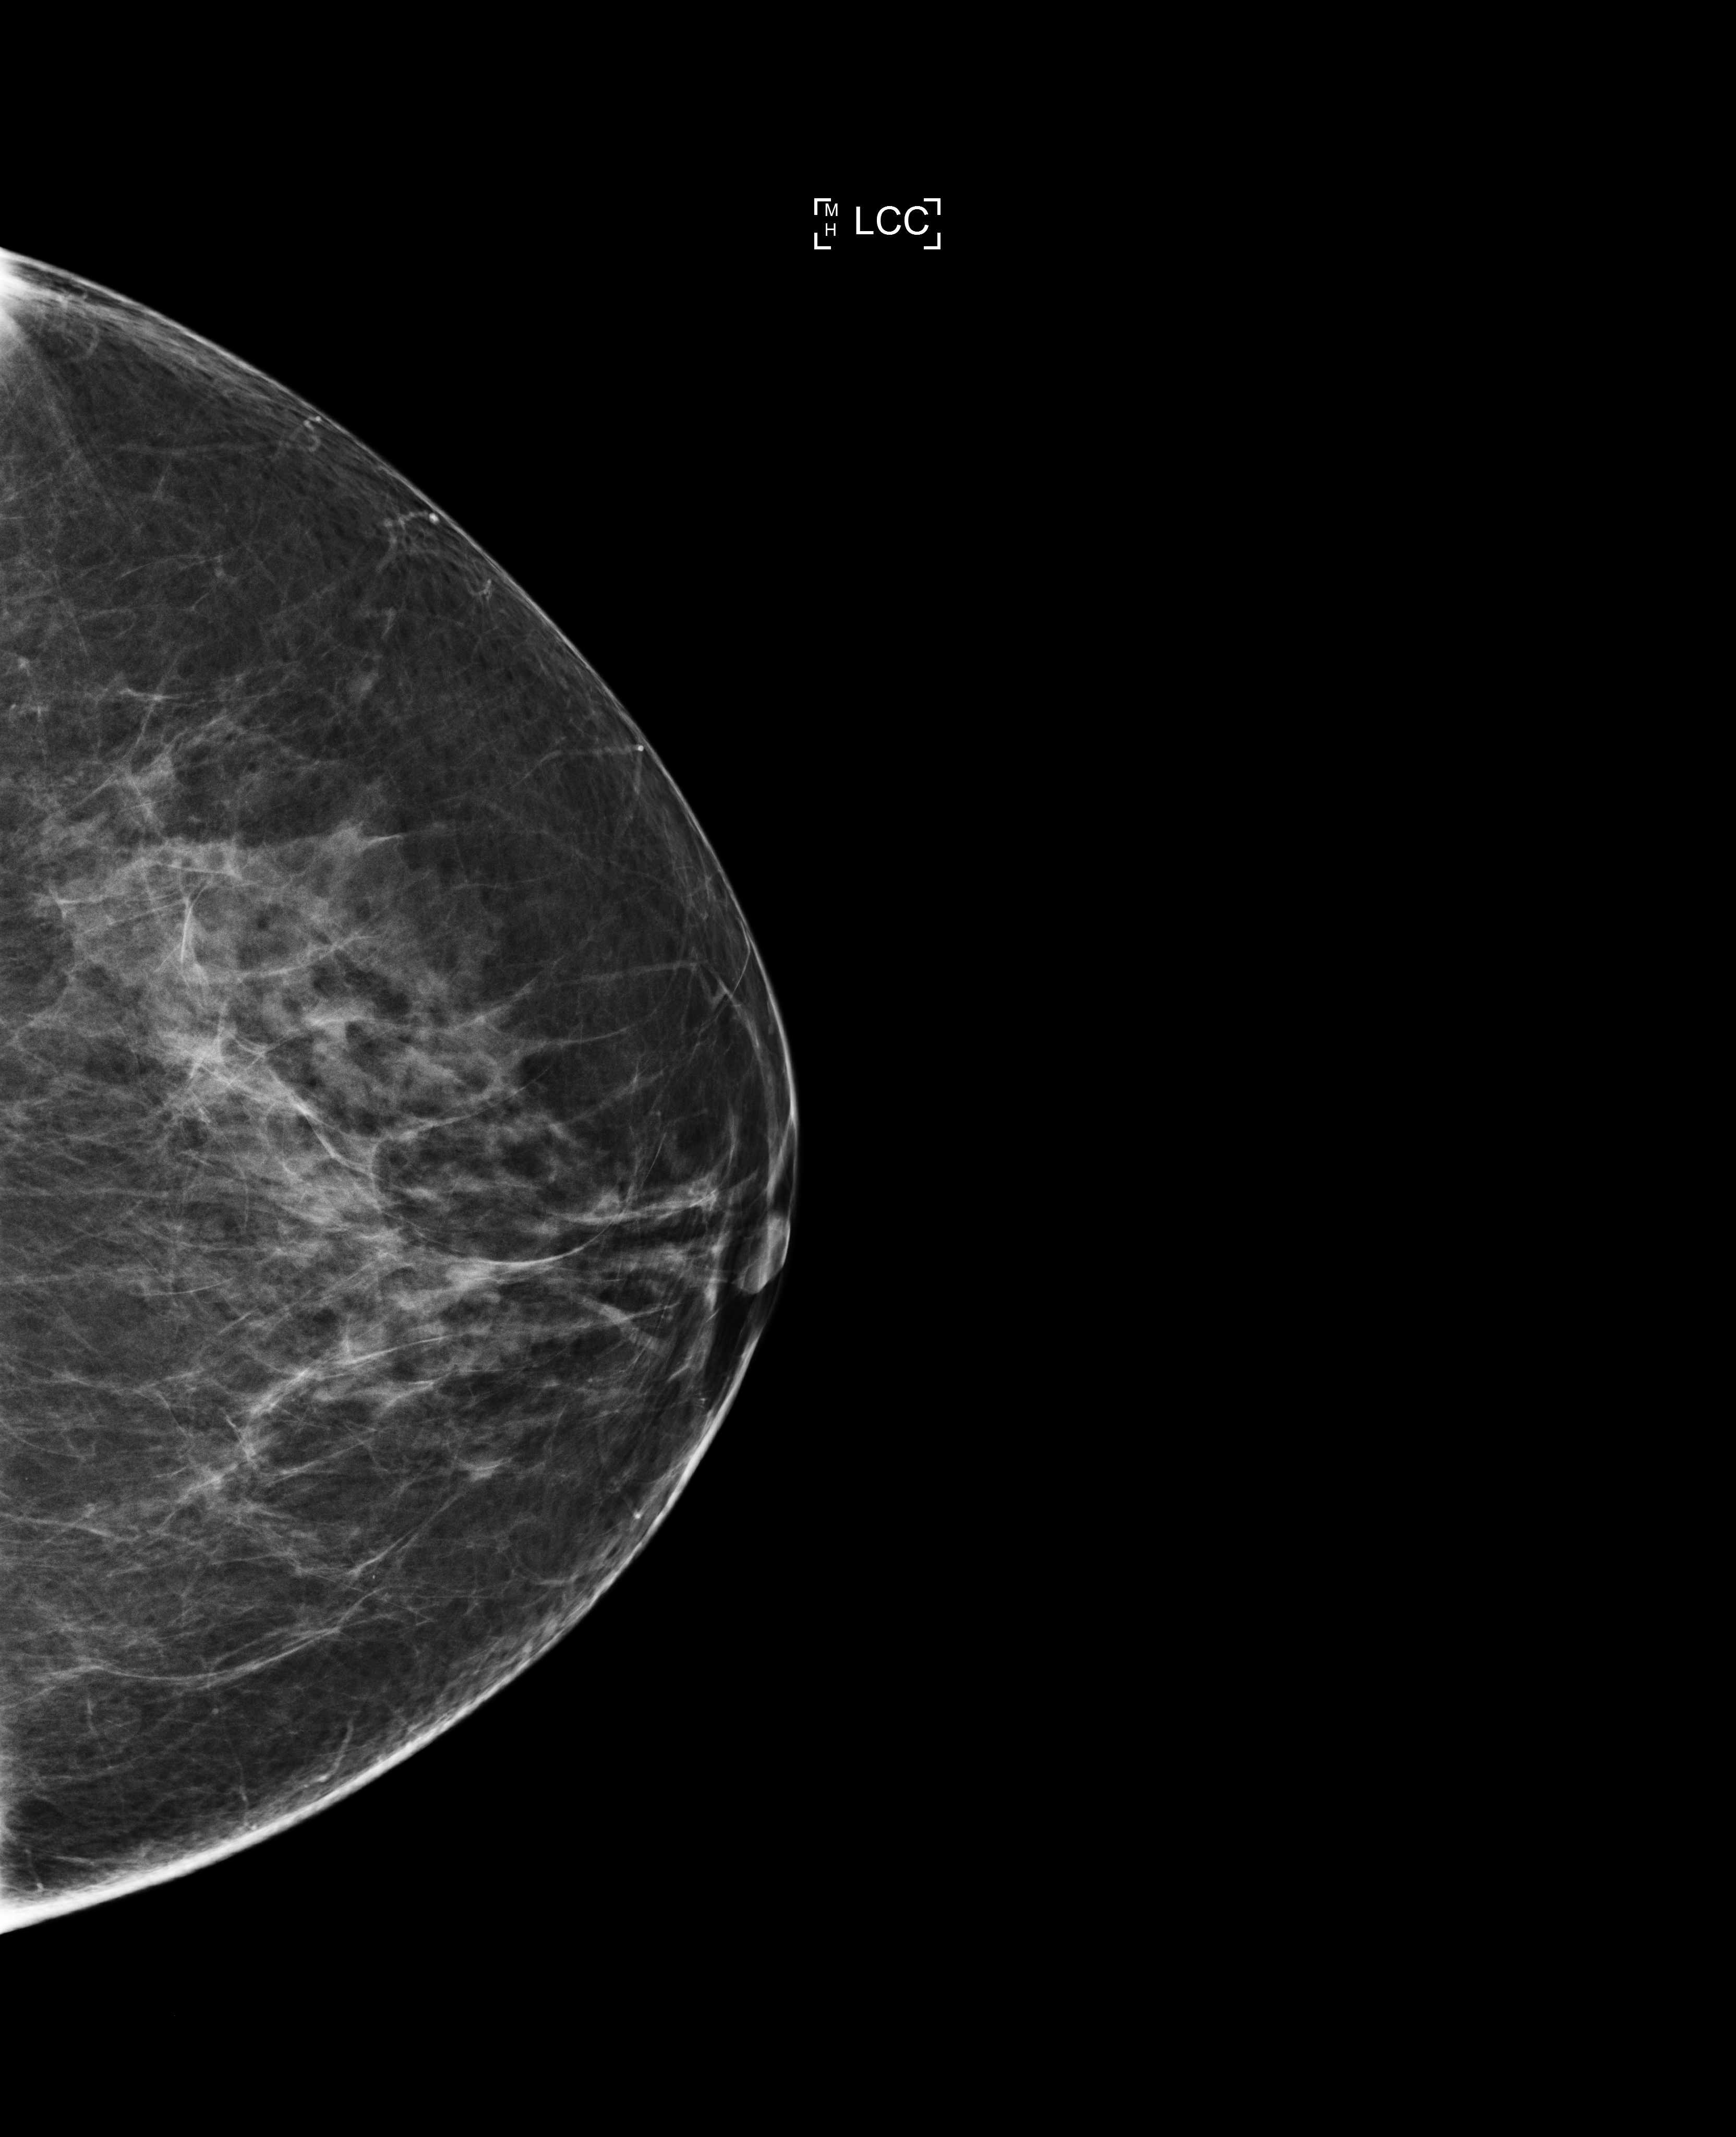
Screening examination, system: Selenia Dimensions. Female patient, age 57 years.
Image type: full-field digital mammogram. Breast: left. Projection: craniocaudal (CC) view.